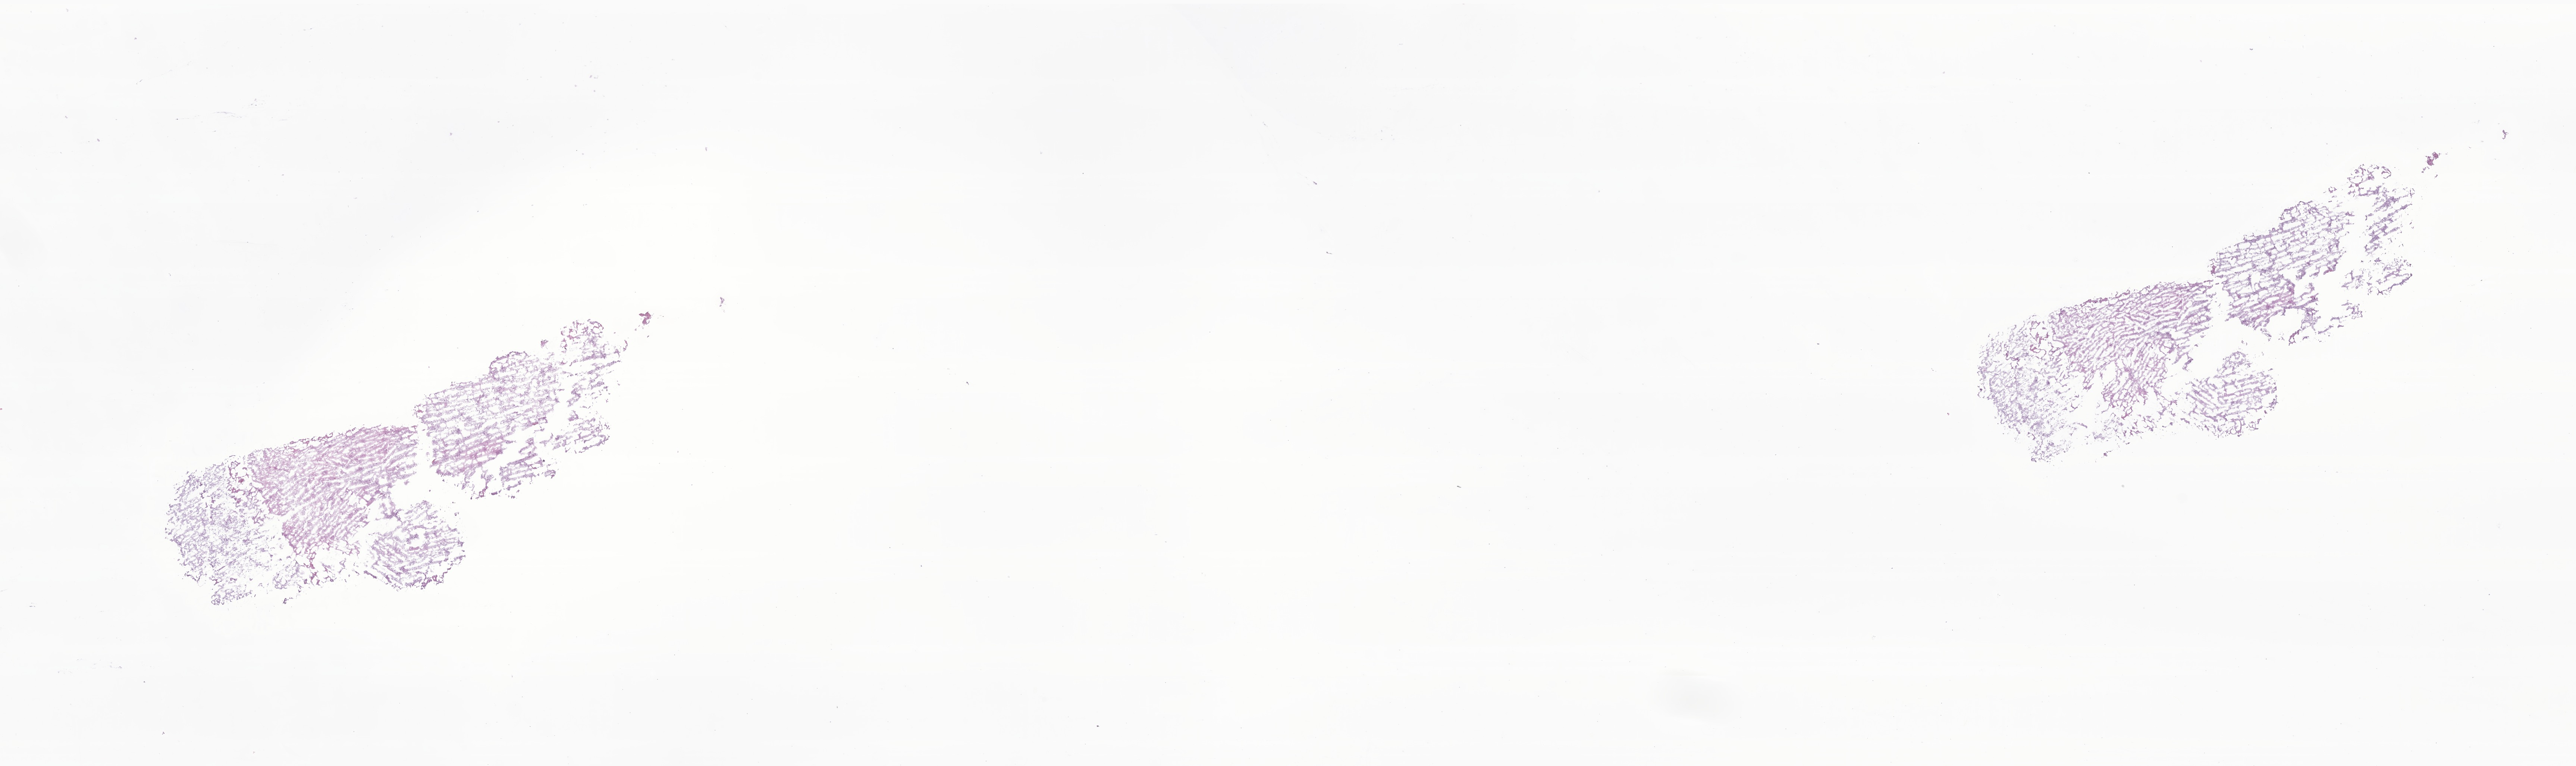
Haematoxylin and eosin whole-slide image of tumor tissue from the brain — whole scanned area (about 29.1 x 8.7 mm) shown as a low-resolution overview, frozen section (OCT-embedded). Patient male; age 92 months.
Diagnosis: Pilocytic astrocytoma.